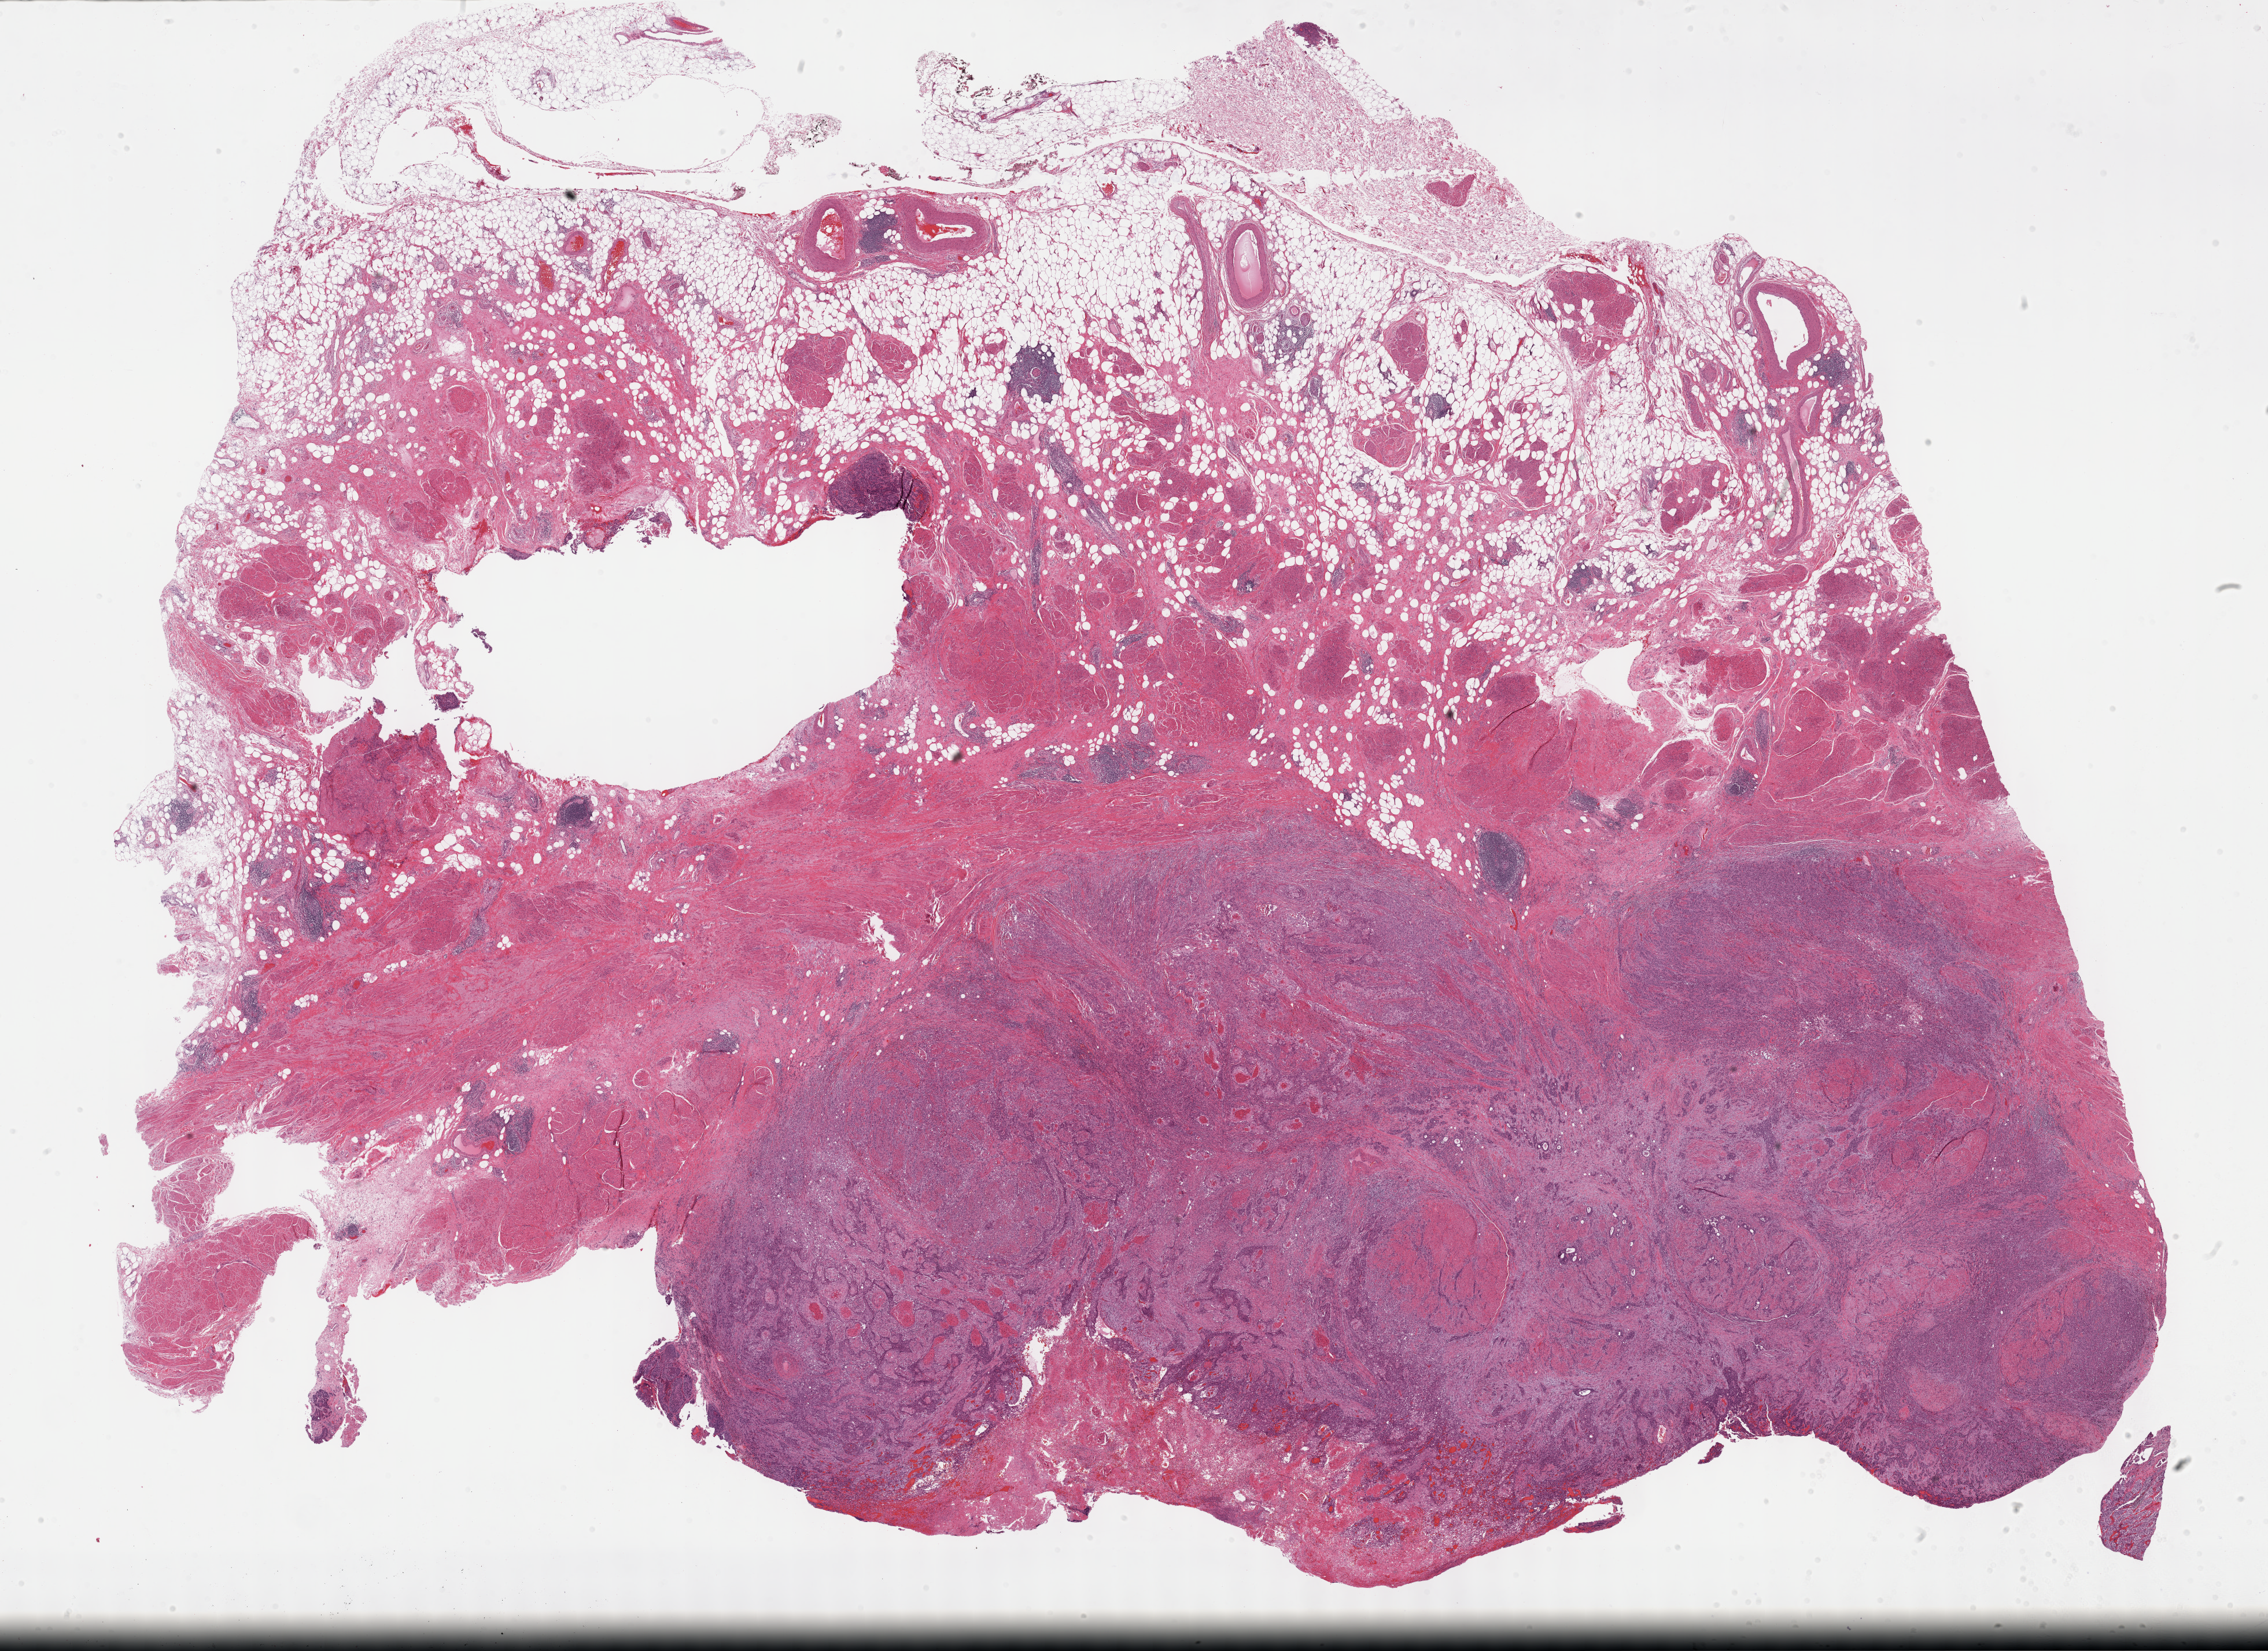
Whole-slide histology image, H&E, low-resolution overview of the scanned area, about 31.7 x 23.1 mm. Formalin-fixed paraffin-embedded (FFPE) diagnostic section. Bladder, primary tumour sample. Male patient; age at initial diagnosis 57 years. Histologic grade: high grade.
AJCC pathologic stage: II. Diagnosis: Transitional cell carcinoma. Lymph nodes positive (case pathology): 0 of 34 examined. TNM: T2b N0 MX.